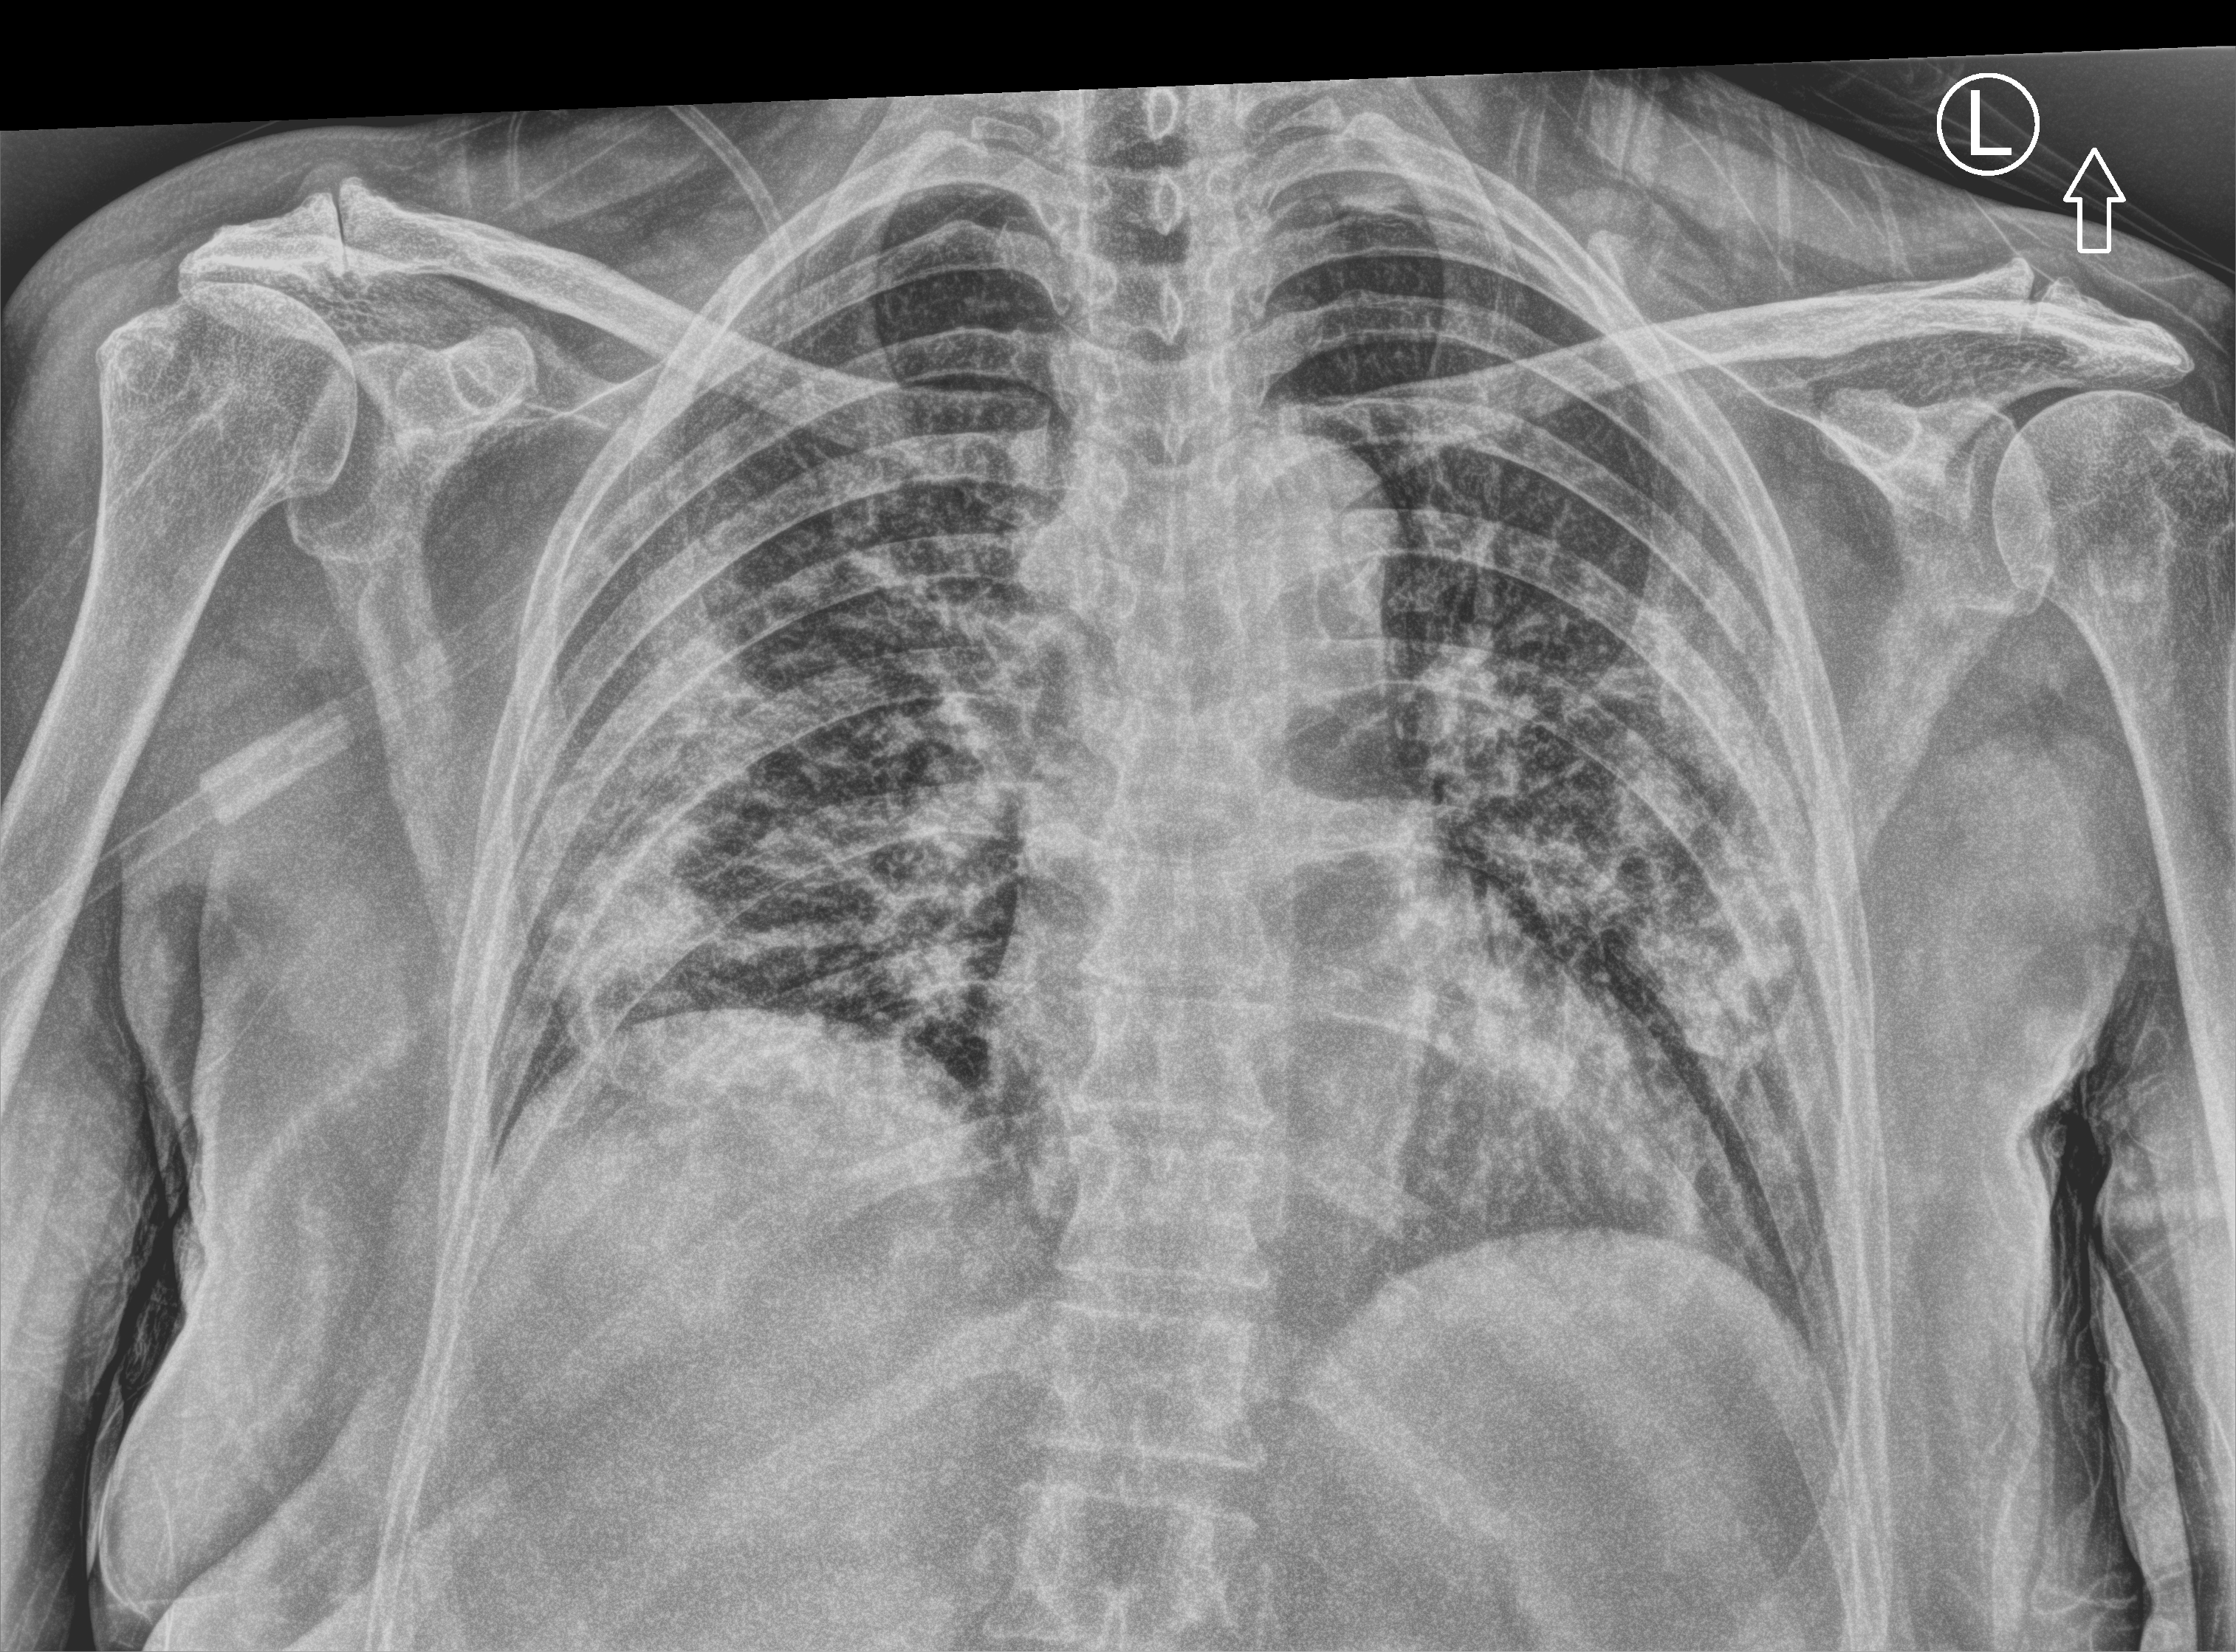
Chest X-ray (portable), anteroposterior (AP) projection. Female patient hospitalised with COVID-19, age 60–74 years.
Hospital-stay facts (about this admission, not read from this image; timing relative to this image not recorded): admitted to intensive care during this hospital stay: yes; mechanically ventilated during this hospital stay: yes.